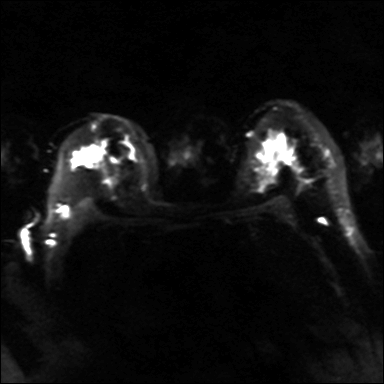
Breast MRI, one axial slice. Slice 22 of 36 in the series (ordered by position). Diffusion-weighted series; image 2 of 4 stored at this slice position (different b-values; order by instance number). 3 T. 4 mm slice thickness. 384 × 384 image matrix, field of view 320 × 320 mm. Female patient.
Outlined on this slice (outlined manually by an expert reader):
- tumour on diffusion-weighted imaging: bounding box <75,146,104,166> (left, top, right, bottom; pixels)